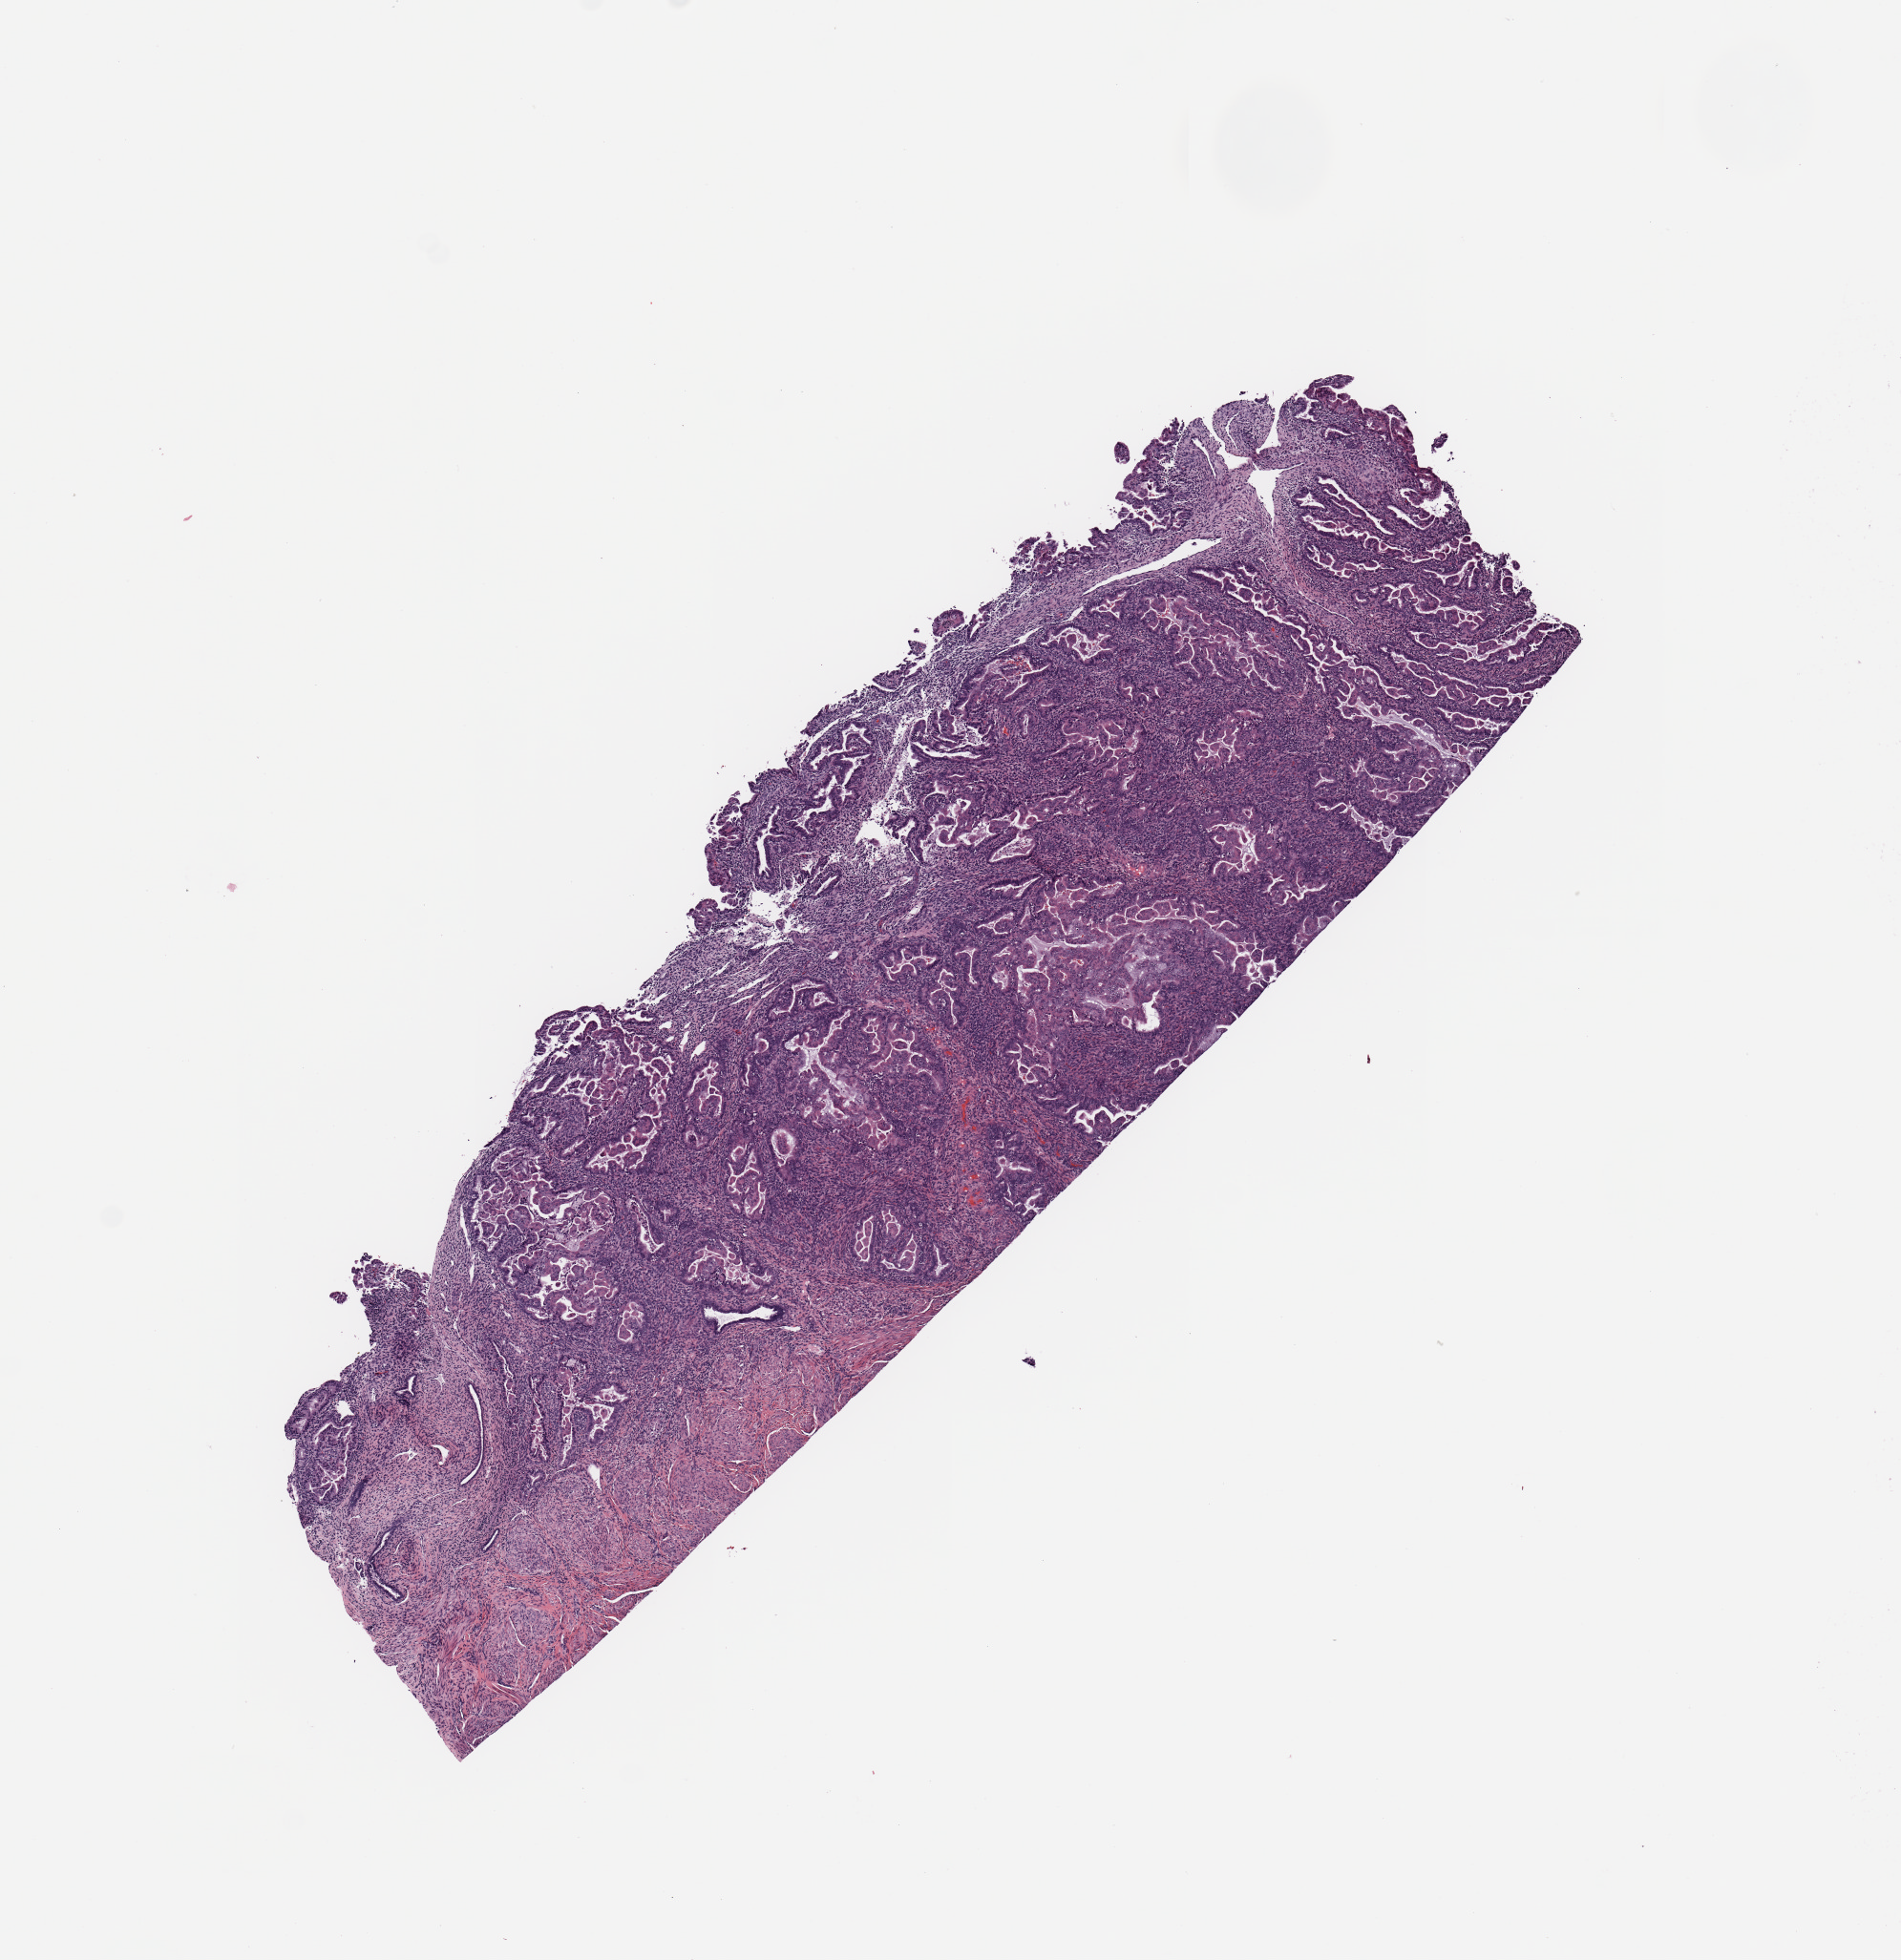
H&E whole-slide image, whole scanned area (about 7.9 x 8.1 mm) shown as a low-resolution overview. Tumour tissue sample, sampled site: uterus. Female, 42 y/o. Histologic grade: G1 (well differentiated). Pathologist review of this section (percent, as recorded): tumour nuclei 85%, necrosis 0%.
Diagnosis: Endometrioid adenocarcinoma, NOS. AJCC pathologic stage: I. Primary tumour site (as recorded): posterior endometrium.